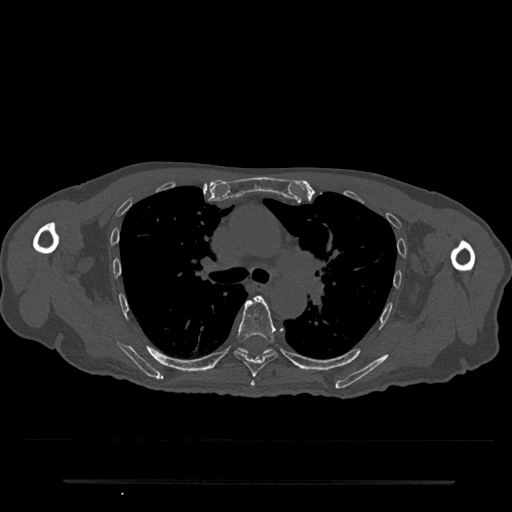
CT including the spine, one axial slice; slice 523 of 797 in the series (ordered by position); reconstruction kernel Br40s/3; 120 kVp; bone window (W 1800 / L 400 HU); 512 × 512 image matrix, field of view 427 × 427 mm. Male patient, age 74 years. From the clinical record (not read from this slice): primary cancer: prostate.
Annotated regions visible in this slice (semi-automatic segmentation, software-assisted and operator-edited):
- T5 vertebra: bounding box <250,381,255,387> (left, top, right, bottom; pixels)
- T6 vertebra: <234,296,277,377>
- T7 vertebra: <239,348,273,359>